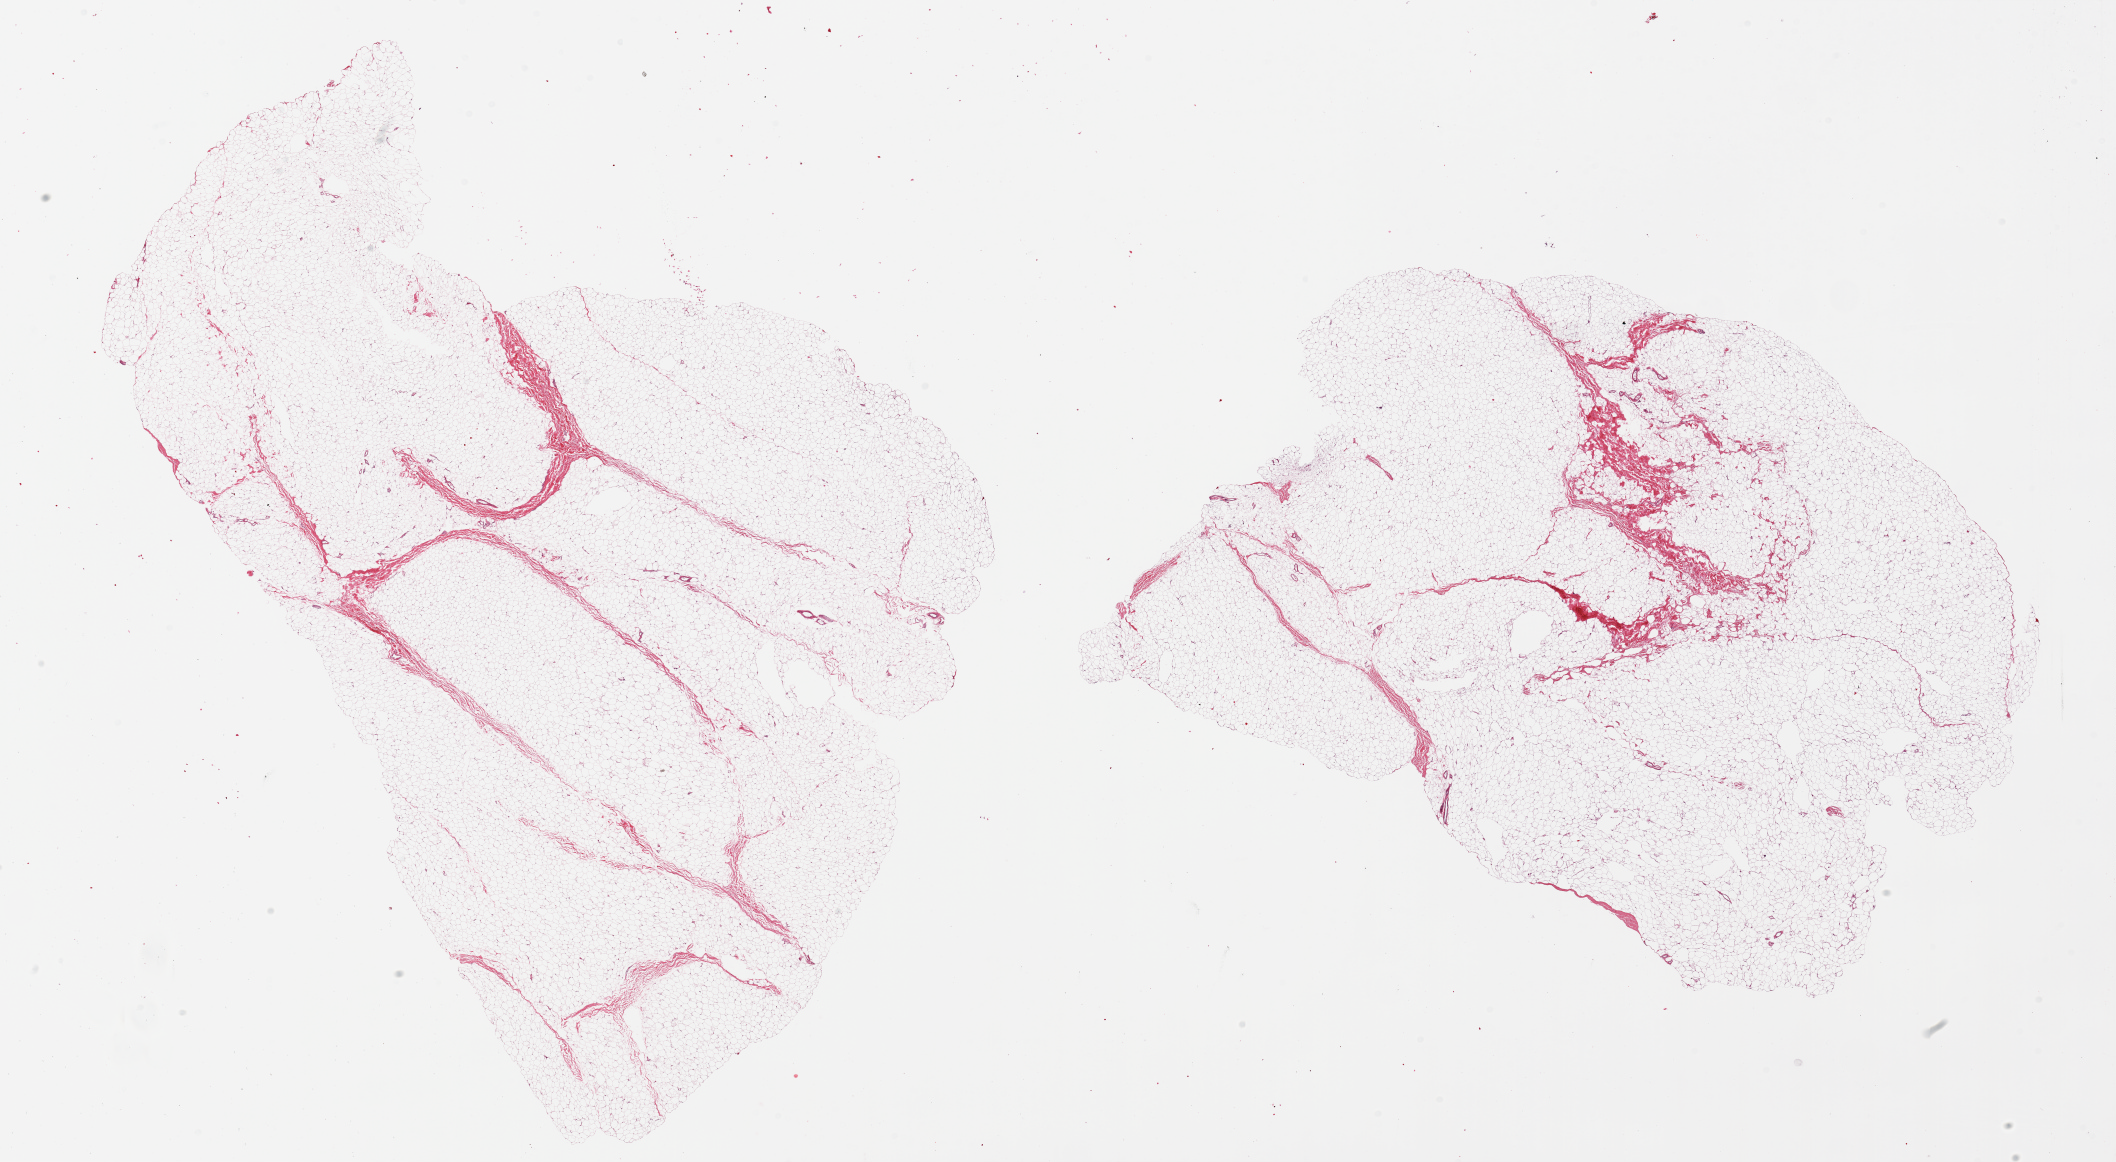
Whole-slide image, hematoxylin and eosin (H&E) stain — shown as a low-resolution overview of the whole scanned area (about 33.5 x 18.4 mm, acquisition: 20x scan). PAXgene-fixed paraffin-embedded (PFPE) section. Target tissue: breast. Donor tissue sample. Donor sex: male.
* review note (as recorded): 2 pieces, adipose tissue with ~5% fibrous tissue, no ductal elements identified